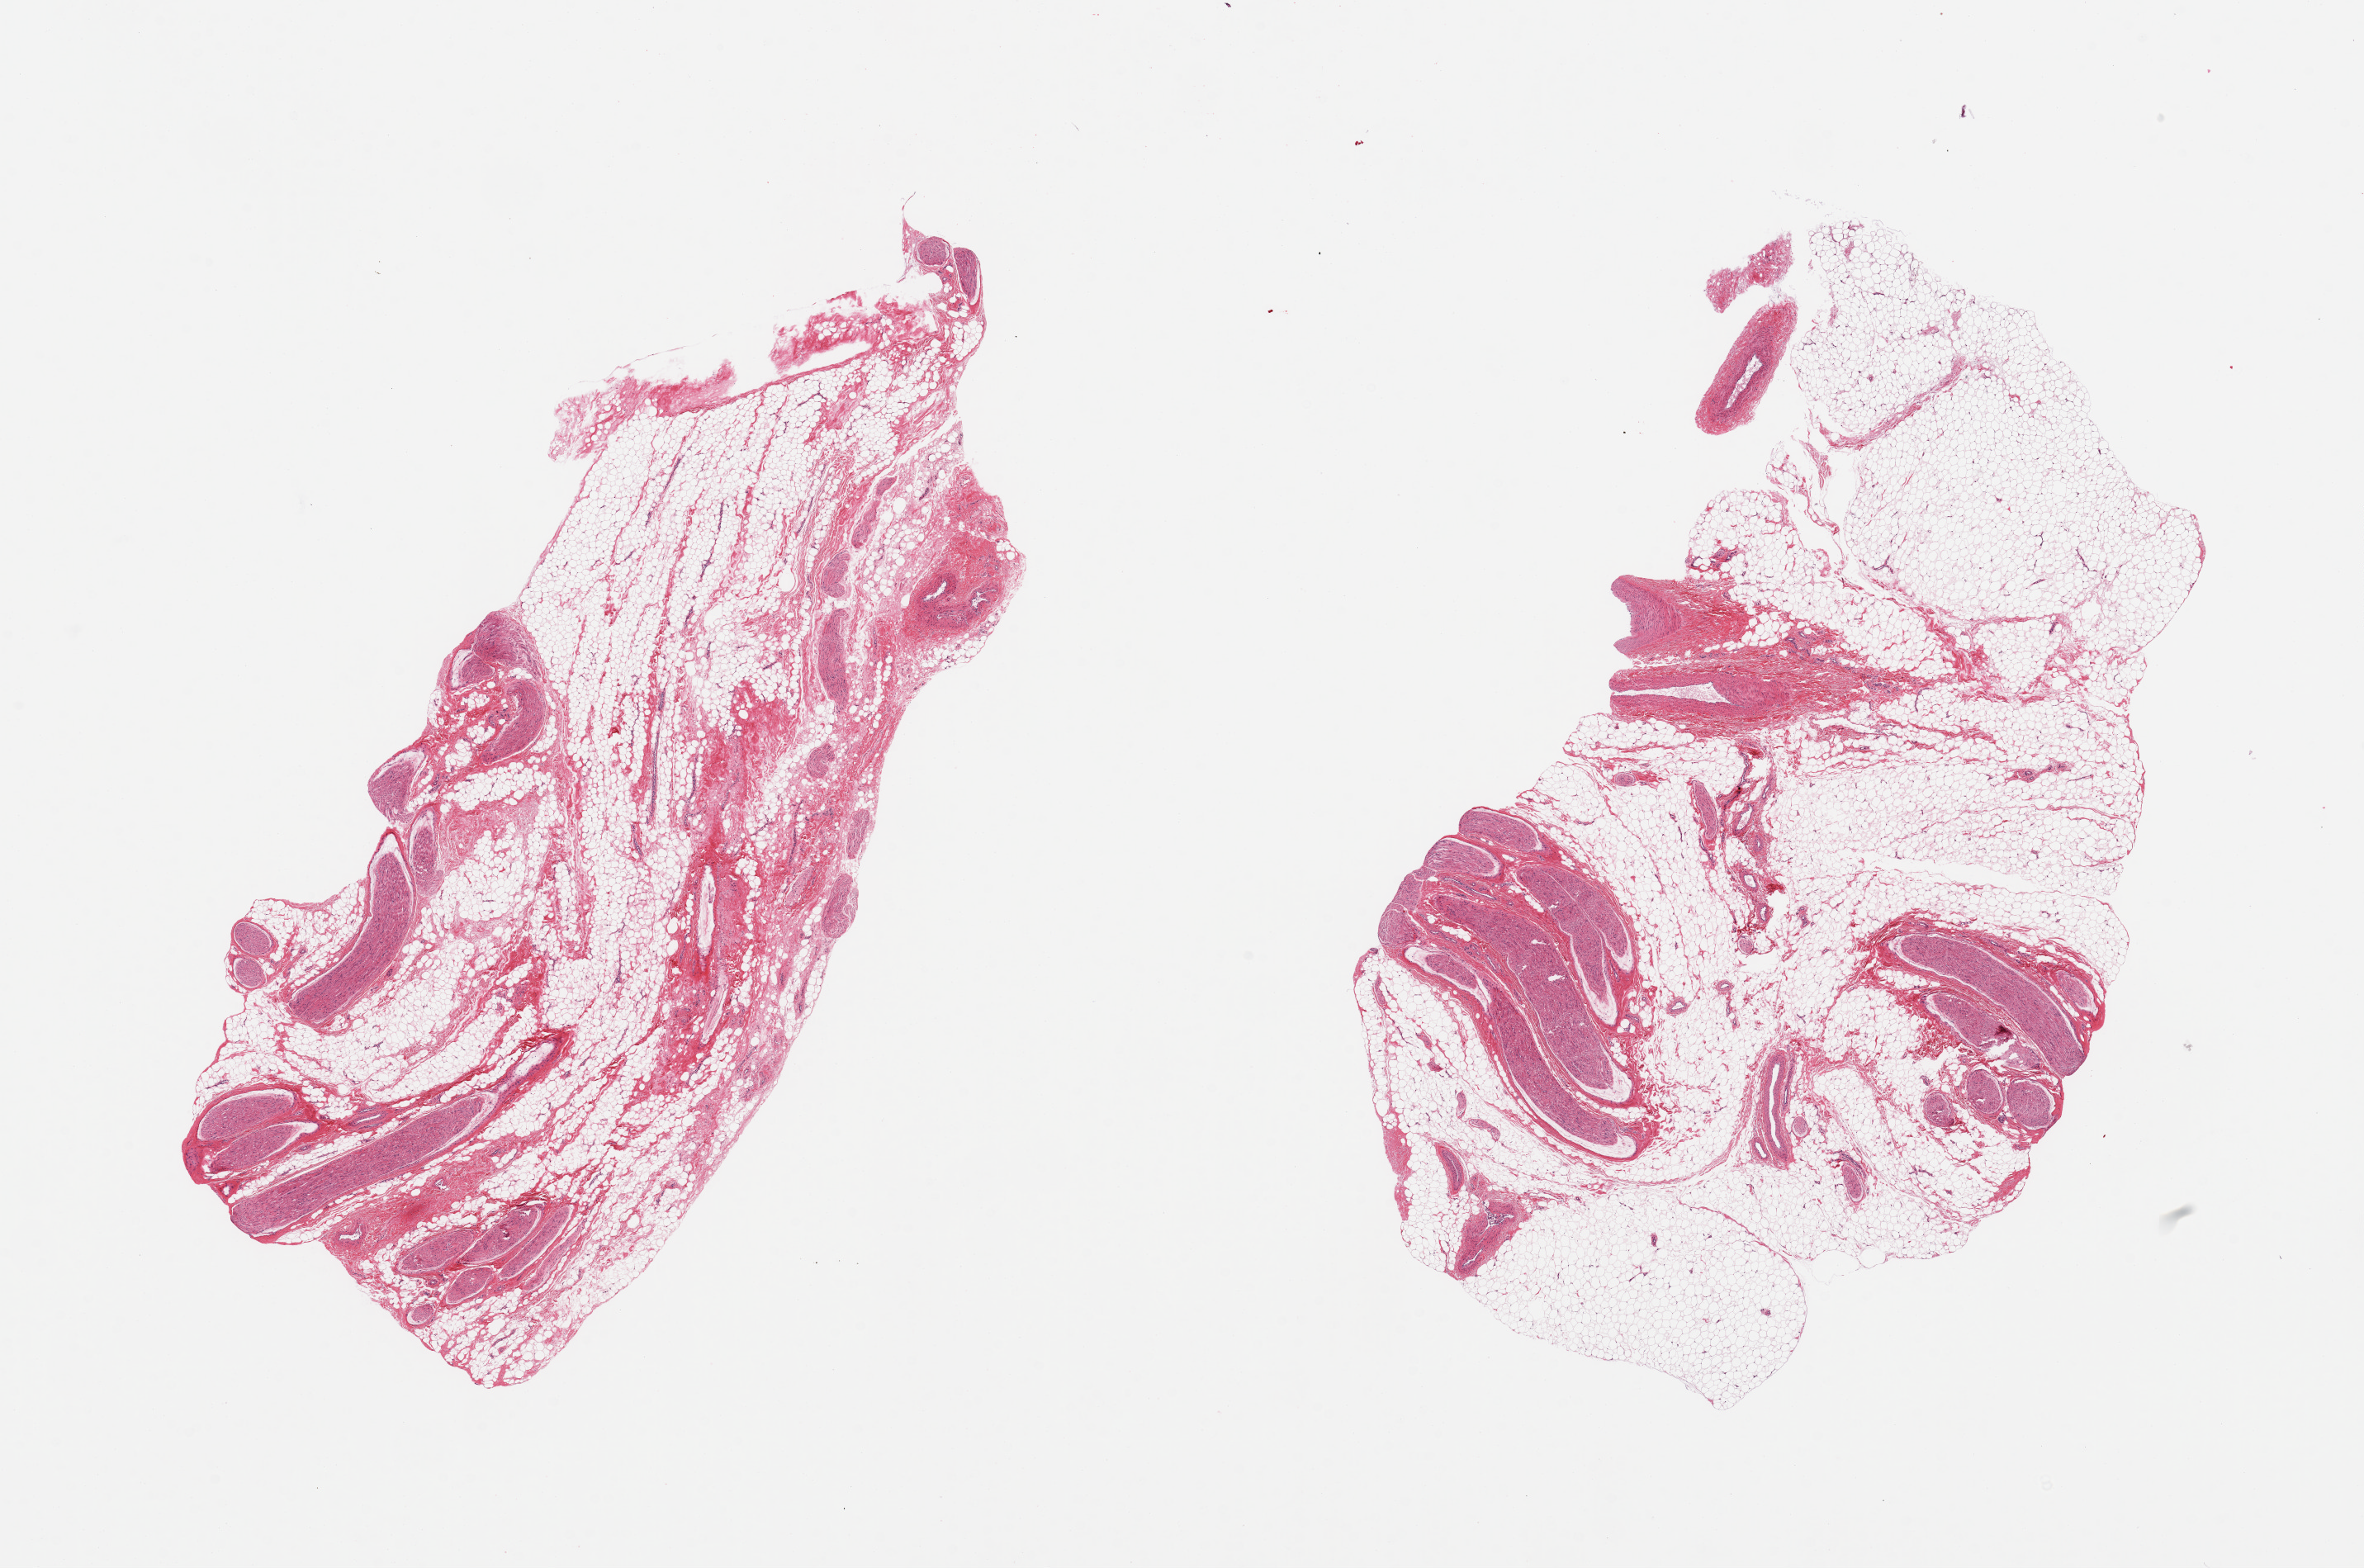
Digitized hematoxylin and eosin (H&E)-stained section, brightfield — shown as a low-resolution overview of the whole scanned area (about 22.6 x 15.0 mm); PAXgene-fixed paraffin-embedded (PFPE) section; target tissue: adipose tissue; tissue donor sample. Donor sex: female.
* reviewer comment on this tissue sample: 2 pieces; contains 30% blood vessels & nerves